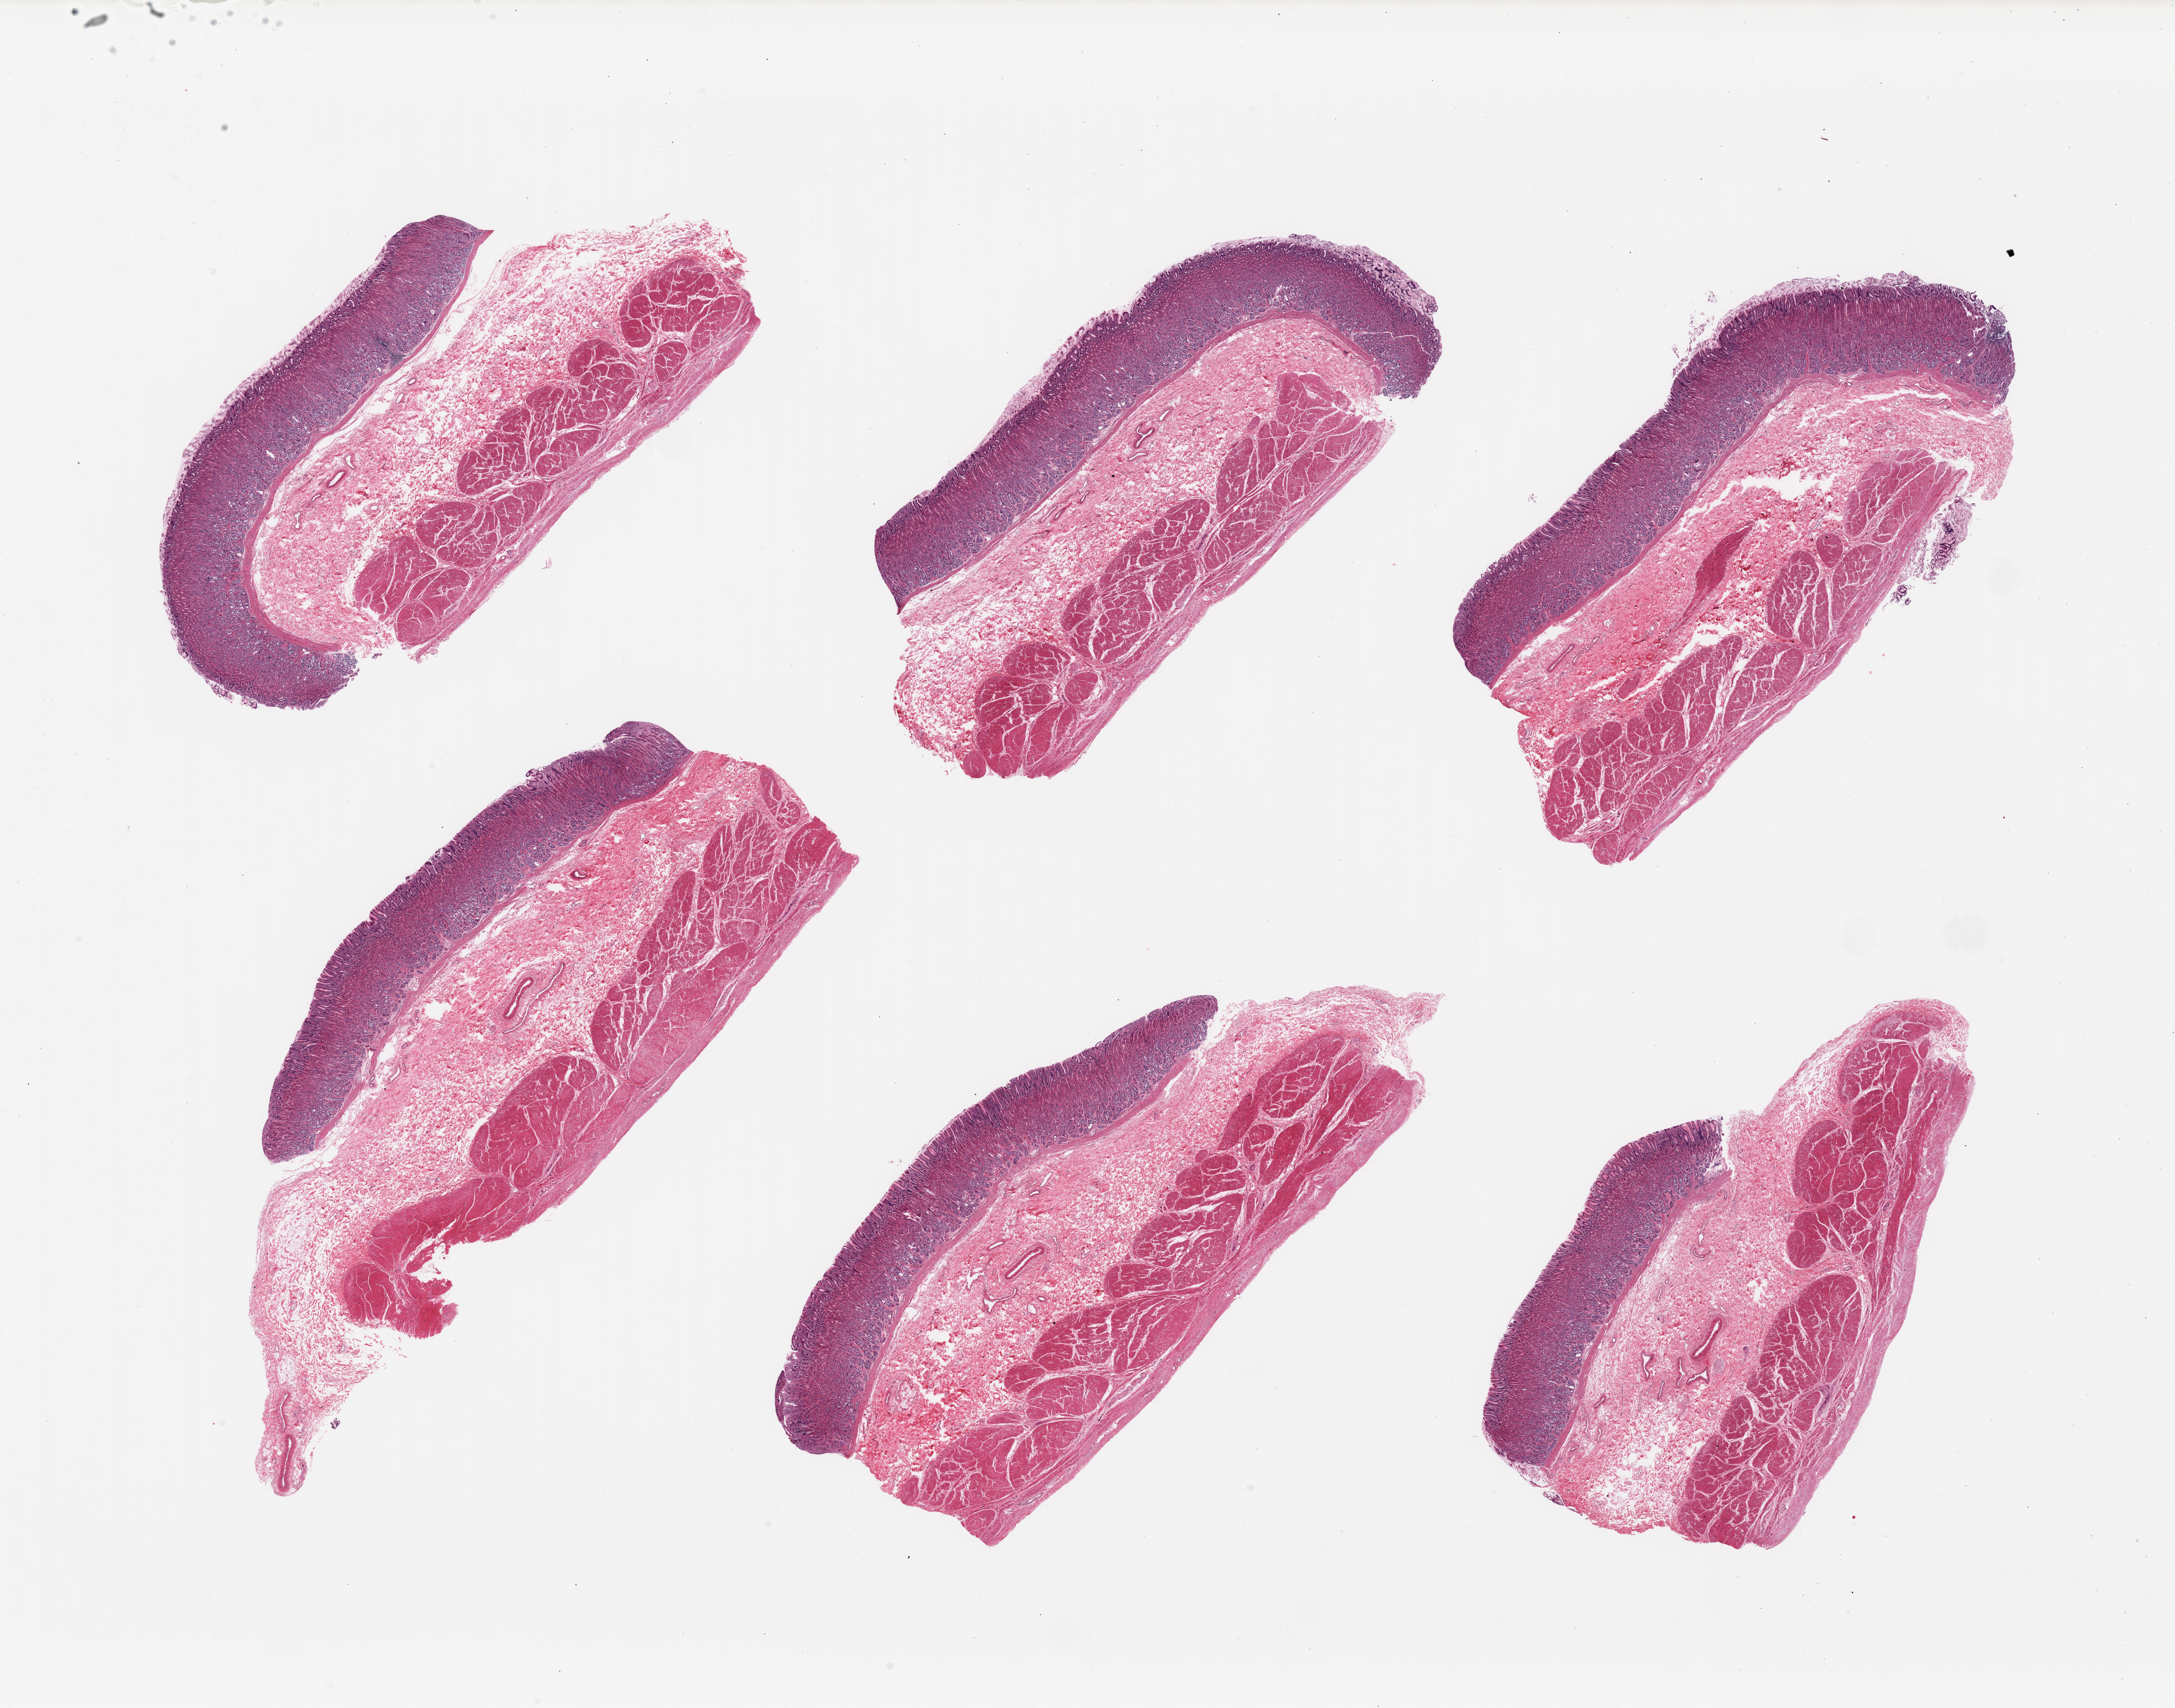
Digitized H&E-stained section, whole scanned area (about 29.5 x 23.2 mm, slide scanned at 20x) shown as a low-resolution overview; PAXgene-fixed, paraffin-embedded tissue; sampled site (target tissue): stomach; tissue donor sample. Donor sex: male.
Review note (as recorded): 6 pieces; well dissected, full thickness gastric mucosa and muscularis.